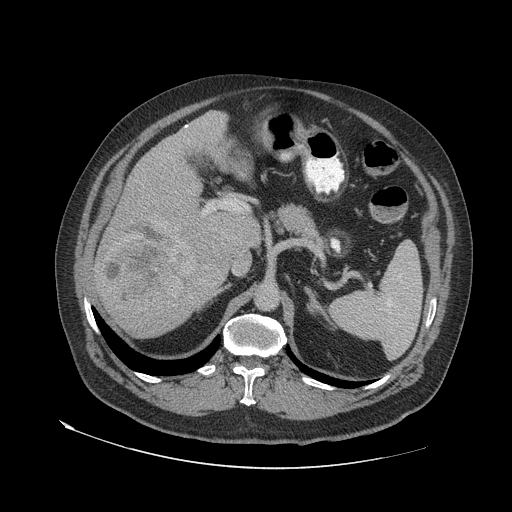
Contrast-enhanced abdominal CT (liver protocol), one axial slice; reconstruction kernel STANDARD; 140 kVp; soft-tissue window (W 400 / L 40 HU); 512 × 512 image matrix. Case-level facts recorded for this patient, not image findings: diagnosis: hepatocellular carcinoma (patient treated with transarterial chemoembolisation; whether this scan precedes or follows treatment is not stated here); TNM stage (as recorded): Stage-IVA; Child-Pugh class: A; tumour differentiation: well differentiated; tumour nodularity: multinodular.
Annotated regions visible in this slice (semi-automatically segmented with operator editing):
- liver parenchyma outside the tumour (the mass and vessels are separate outlines, so this box may not span the whole liver): bounding box (x1, y1, x2, y2) in pixels: (94, 110, 260, 336)
- mass: (96, 220, 198, 314)
- liver vessels: (185, 125, 248, 214)